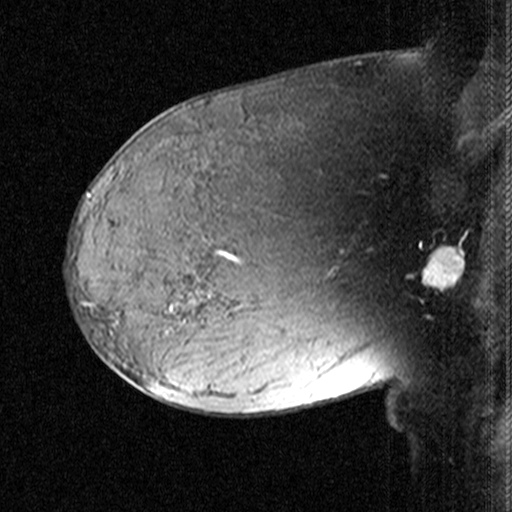
Breast MRI (dynamic contrast-enhanced), one sagittal slice. Position 27 of 44 along the scan axis. Dynamic contrast-enhanced study with each time point stored as its own series, time point 2 of 3 at this slice position (early post-contrast, ordered by acquisition time). 1.5 T. TE 4.5 ms, TR 11 ms. 512 × 512 image matrix, field of view 200 × 200 mm. Patient: female, 38 years. From the clinical record (not read from this slice): setting: breast cancer imaged before/during neoadjuvant chemotherapy; receptor status: HR-positive, HER2-negative.
Annotated regions visible in this slice (semi-automatic segmentation, software-assisted and operator-edited):
- analysis volume of interest (the breast-tissue region the enhancement analysis was run in; not a lesion): box from (x=170, y=232) to (x=259, y=331) px
- tumour enhancement mask (voxels above the 90 % enhancement threshold inside the analysis volume of interest): (x=199, y=251)–(x=239, y=298)